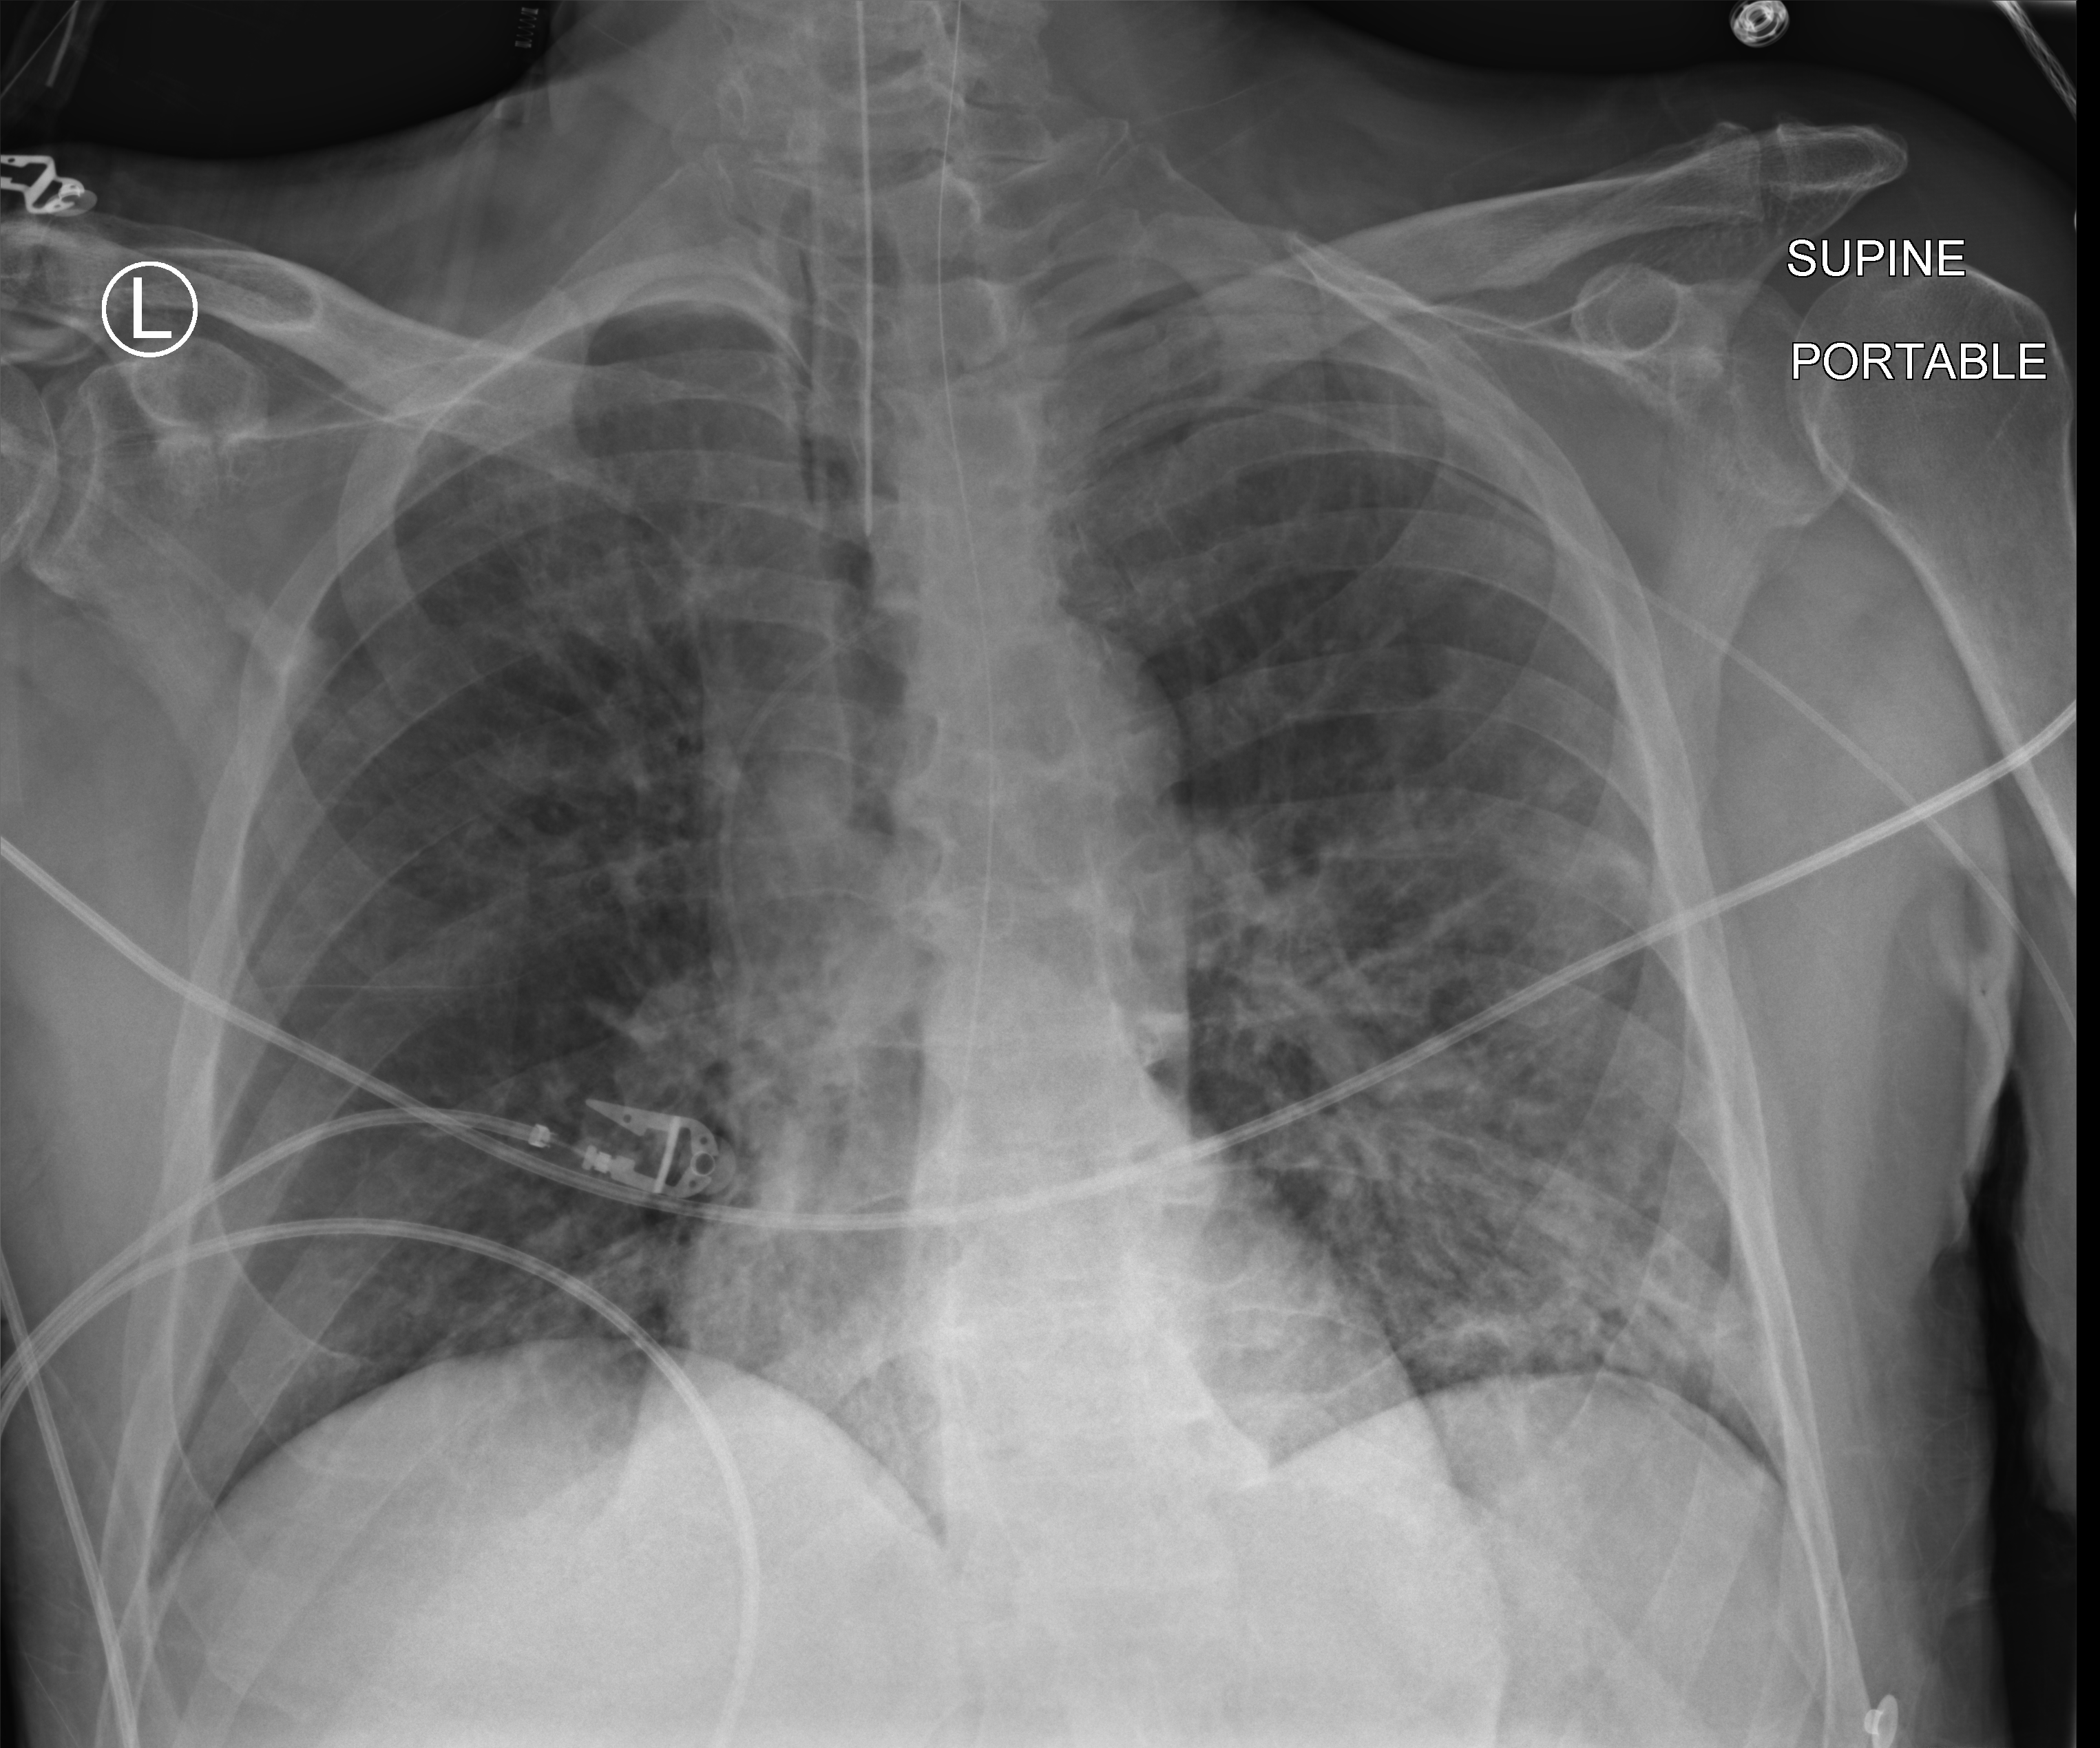
Portable chest radiograph; anteroposterior (AP) projection. Patient hospitalised with COVID-19; male, aged 60–74 years.
Admission-level facts for this patient (not findings on this image; timing relative to this image not recorded):
- smoking status (admission record): never
- mechanically ventilated during this hospital stay: yes